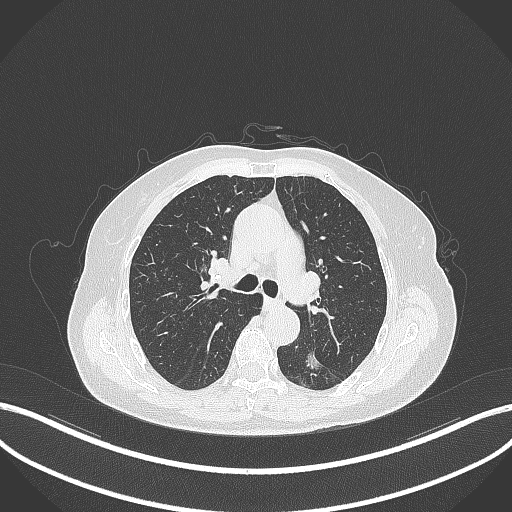
Chest CT, one axial slice. Position 196 of 352 along the scan axis. Reconstruction kernel B70f. Lung window (W 1500 / L -600 HU). 512 × 512 image matrix, field of view 400 × 400 mm. Female patient, age 70 years. Case-level facts recorded for this patient, not image findings: clinical TNM (as recorded): T1c N0 M0.
Structures marked on this image (rectangle marked by the reading radiologist):
- lung tumour (recorded histology: adenocarcinoma): bounding box (x1, y1, x2, y2) in pixels: (301, 346, 328, 378)